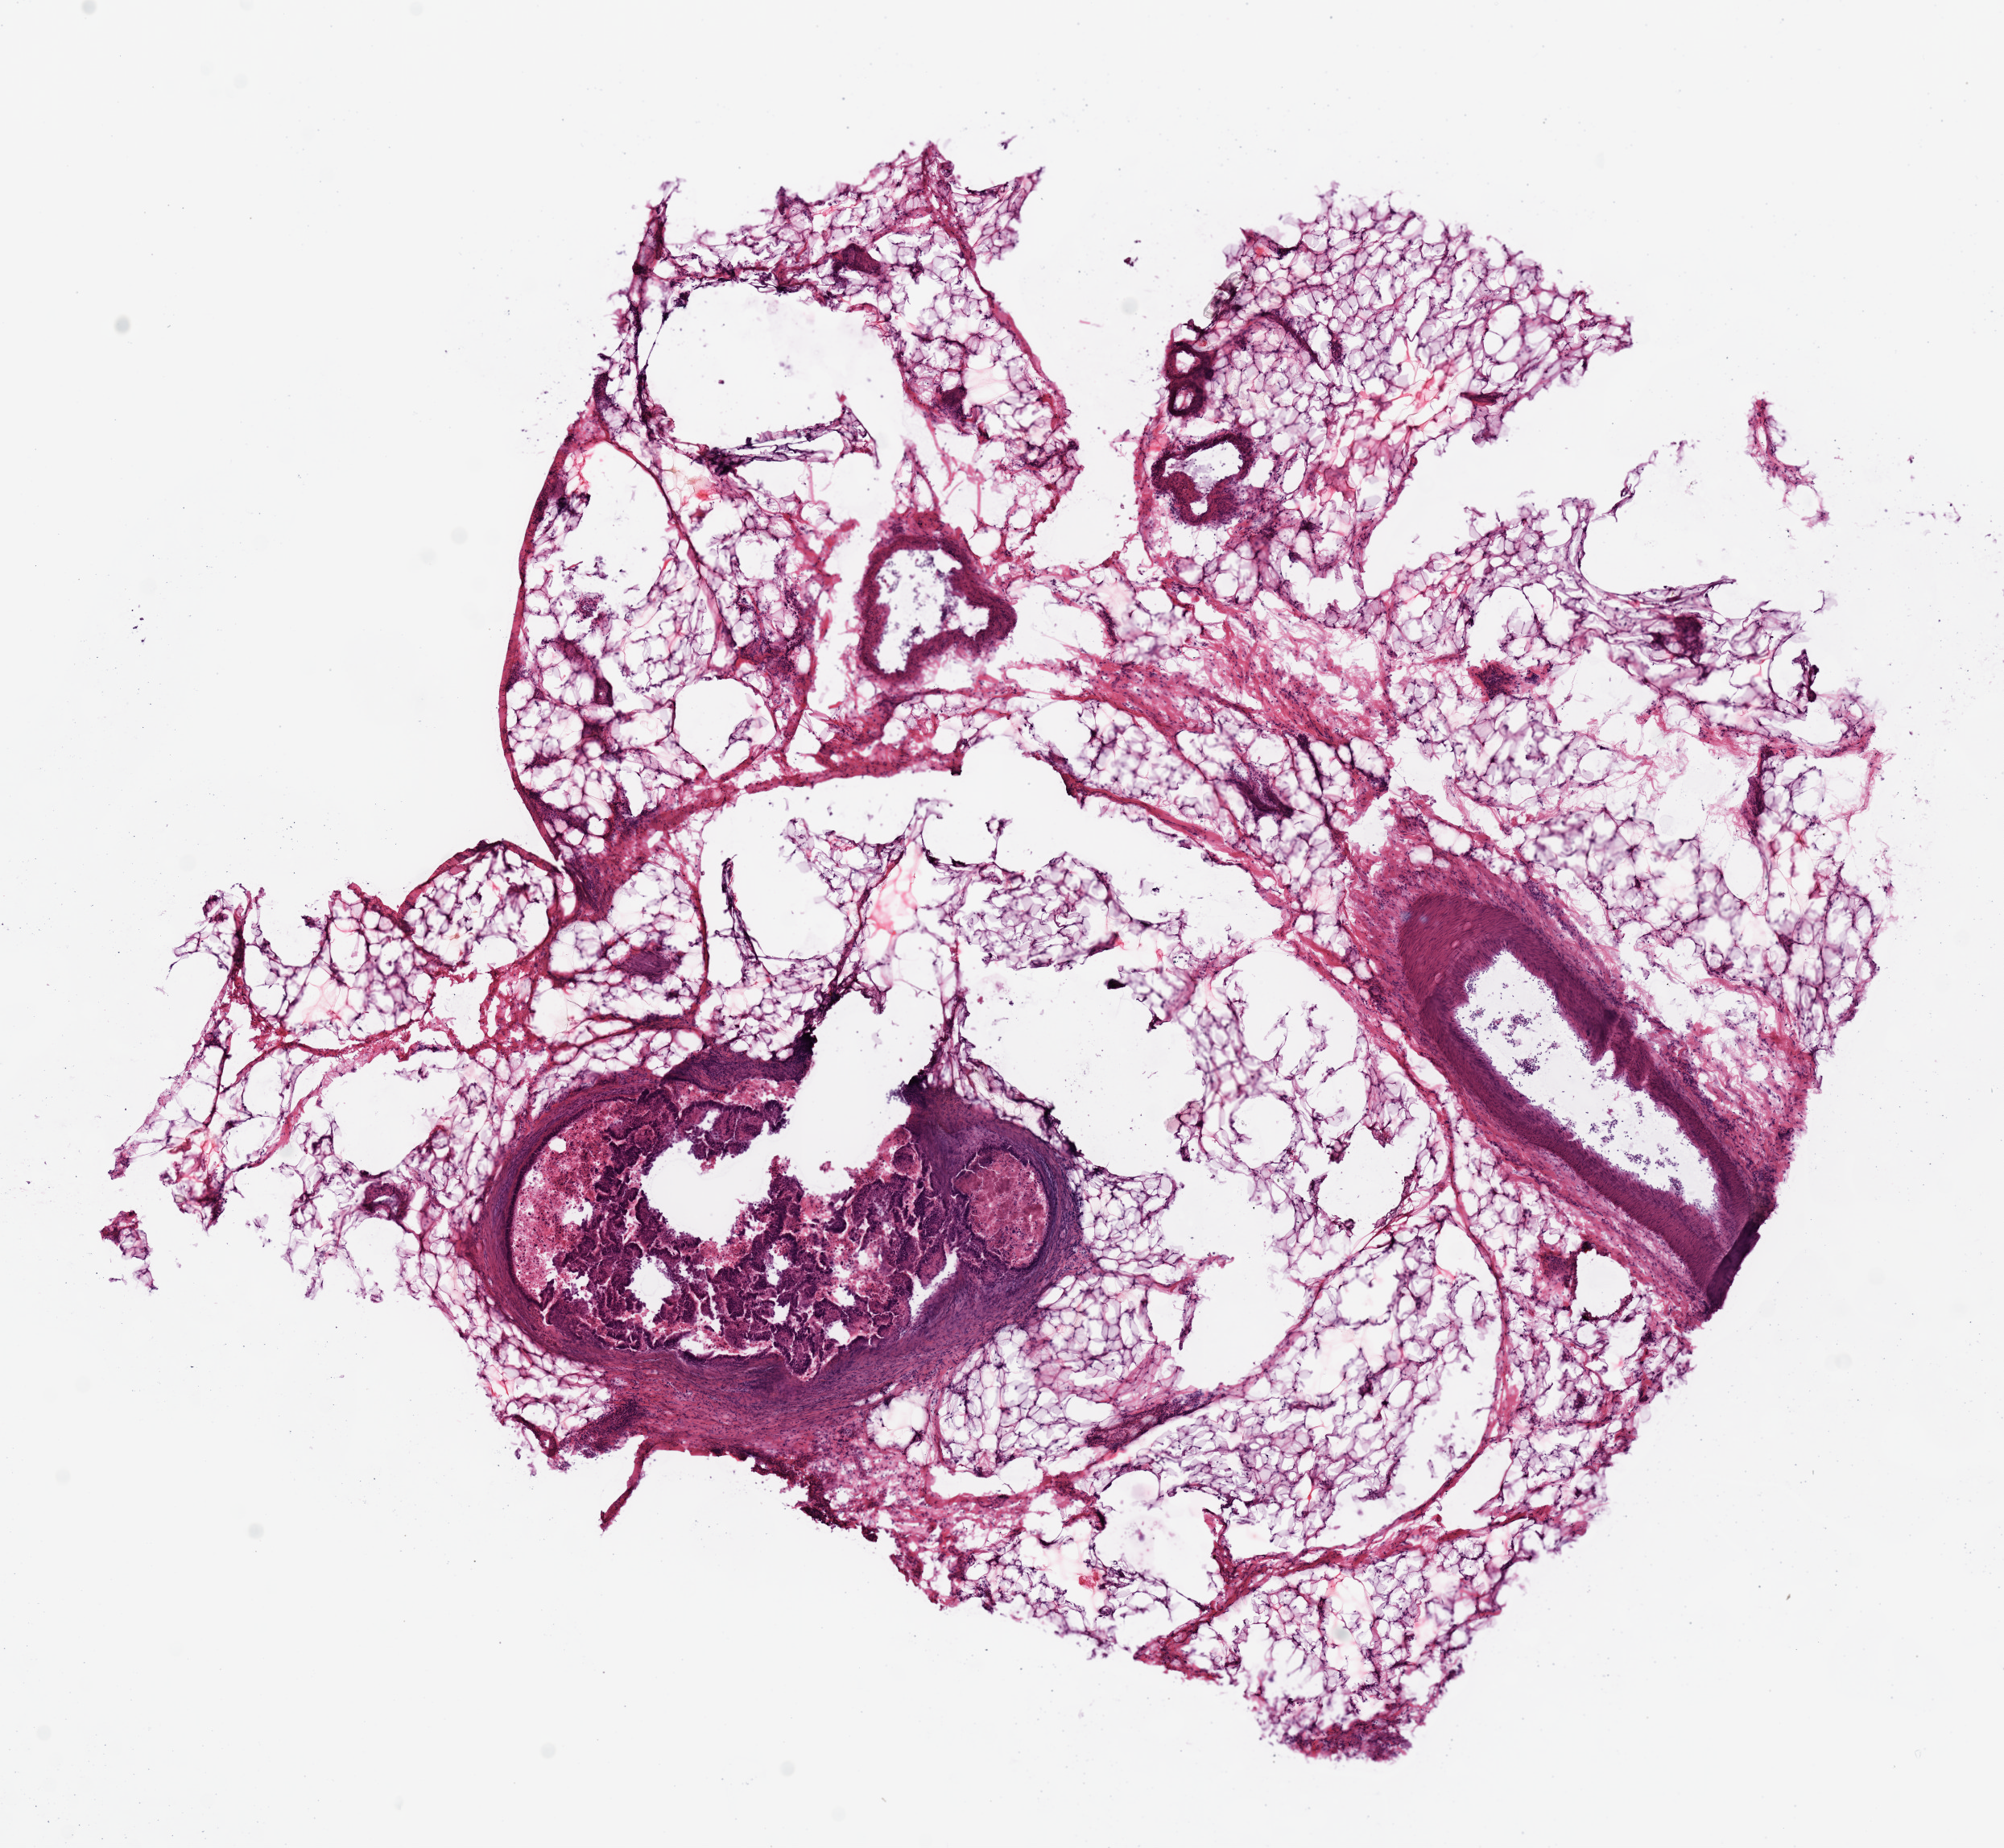
Whole-slide histology image, H&E-stained, whole scanned area (about 9.8 x 9.1 mm, from a 20x scan) shown as a low-resolution overview, frozen section from the top of the tissue portion, stomach, primary tumour sample. Patient: female, age at initial diagnosis 65 years. Histologic grade: G2 (moderately differentiated). Pathologist review of this section (percent, as recorded): tumour nuclei 80%, necrosis 10%.
* lymph nodes positive (case pathology): 2 of 15 examined
* histologic diagnosis: Adenocarcinoma, intestinal type (fundus of stomach)
* AJCC pathologic stage: IIIA (7th edition)